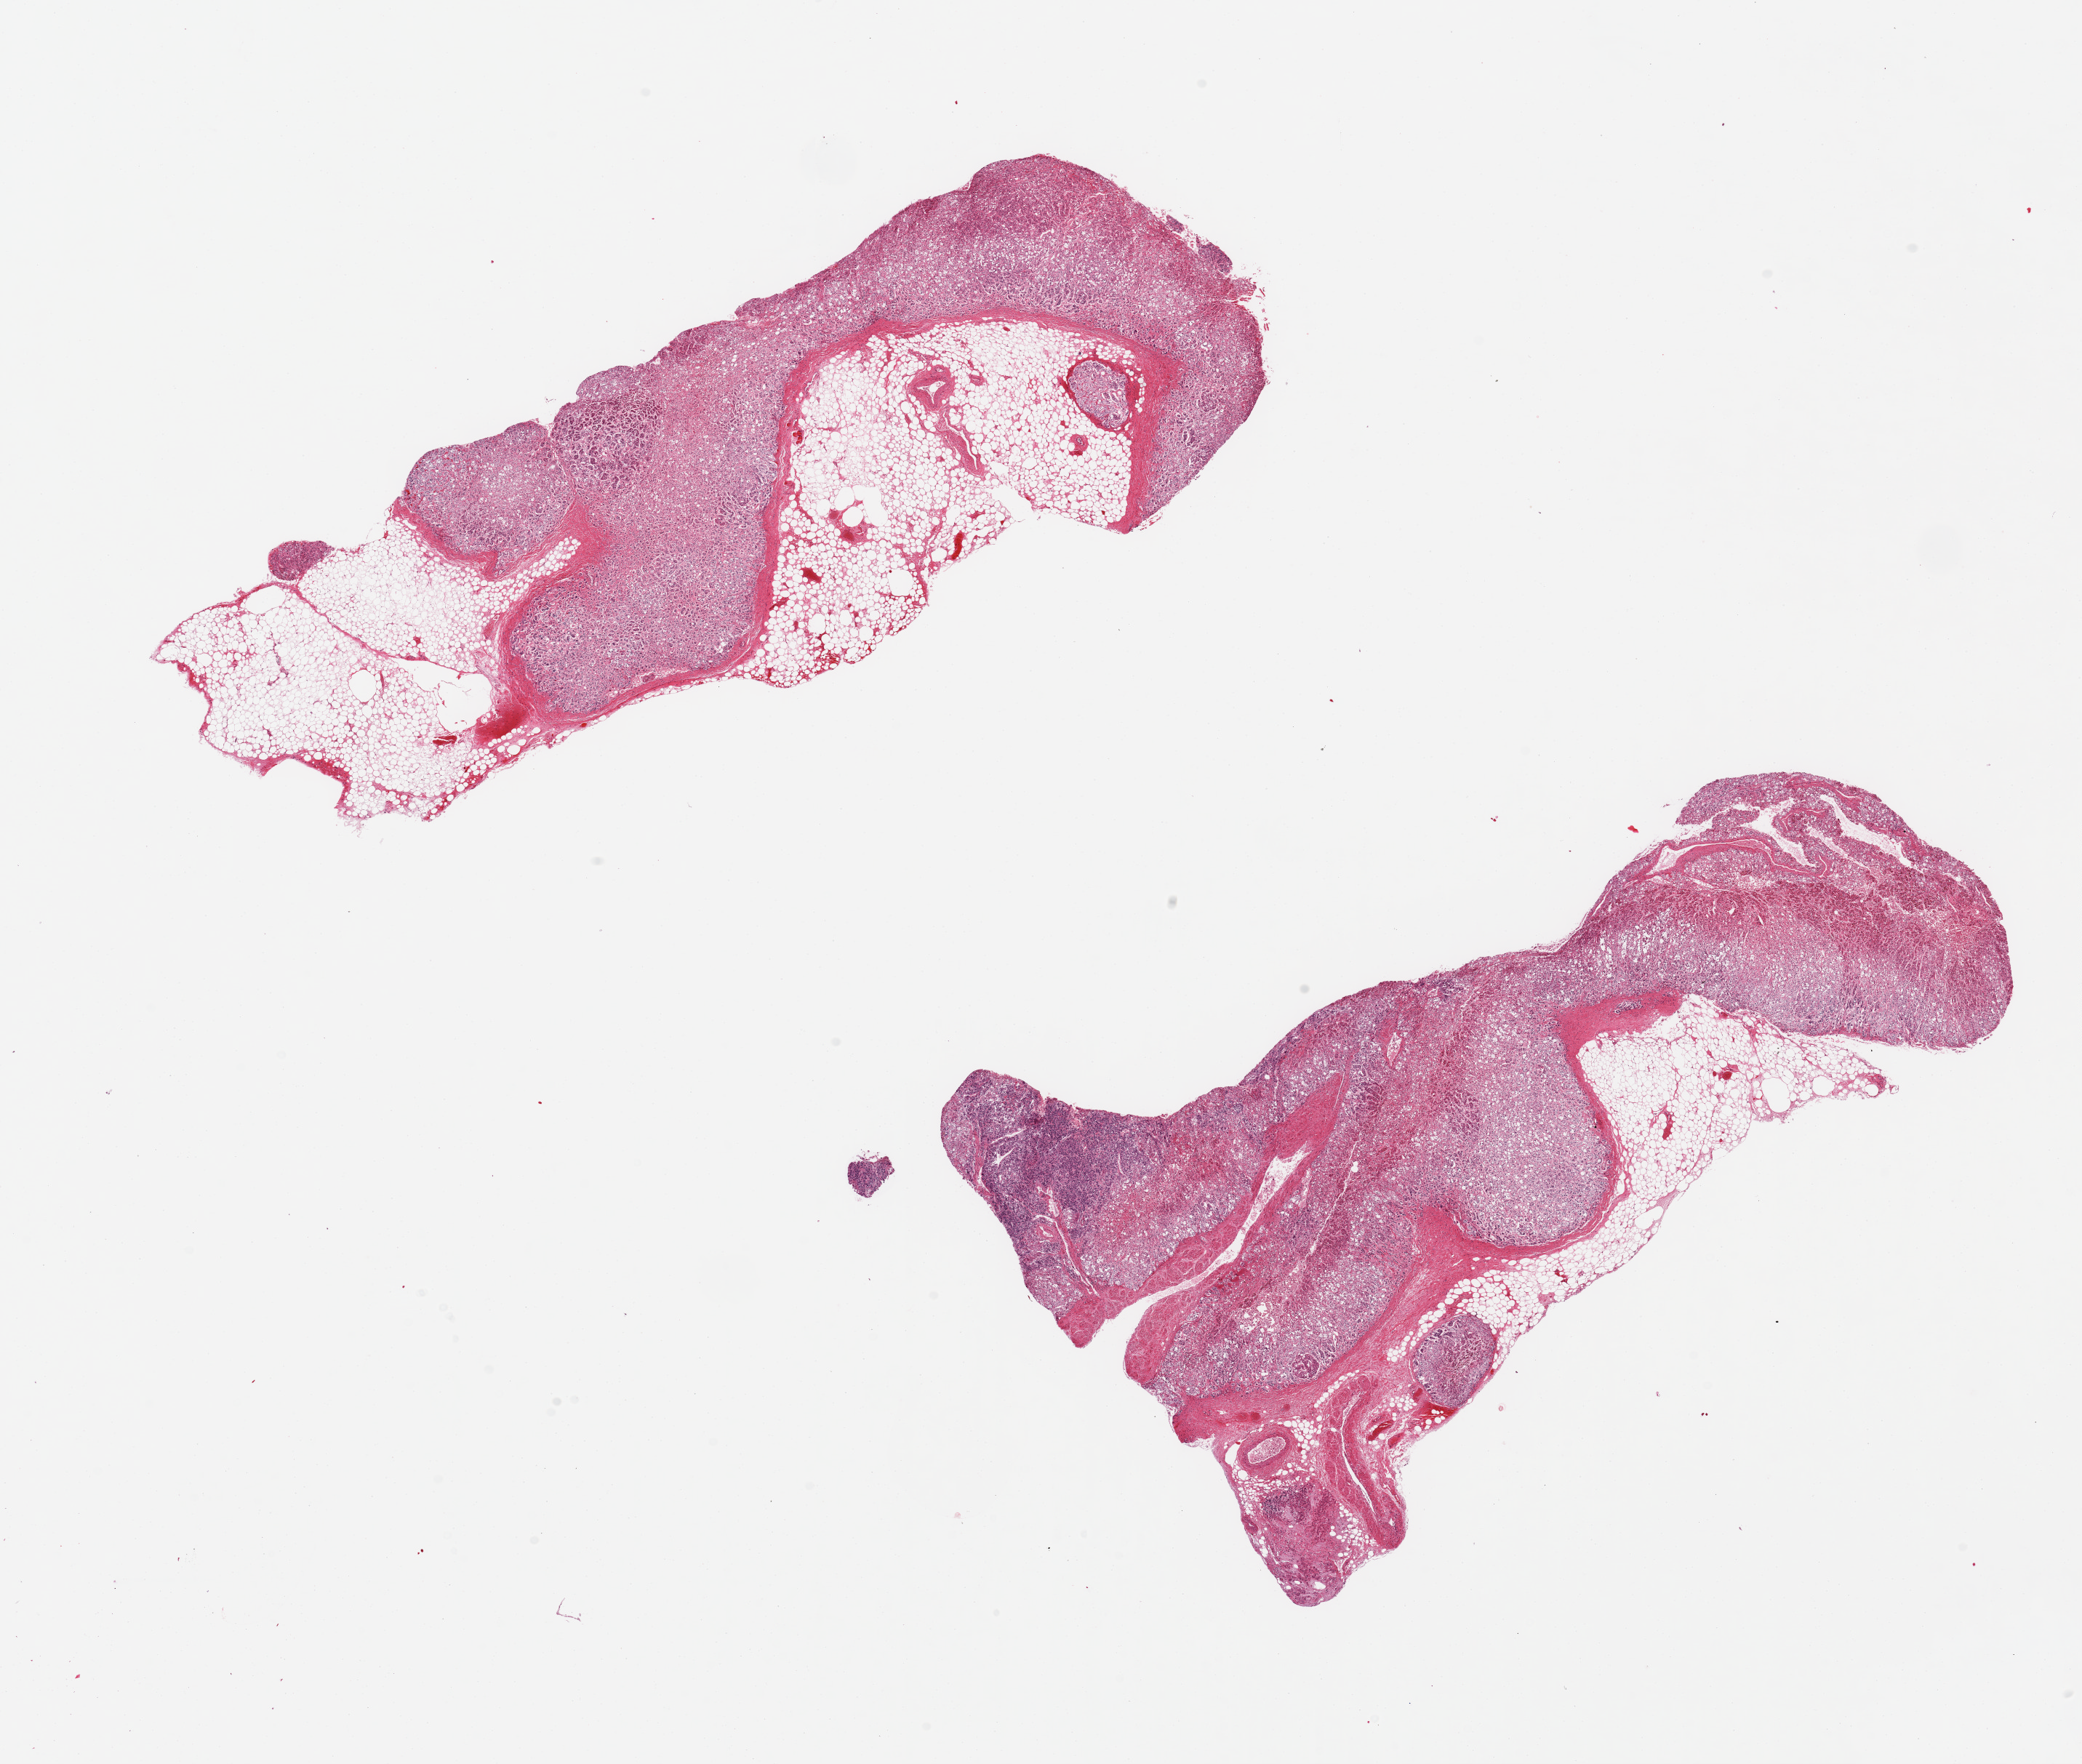
Hematoxylin and eosin (H&E) whole-slide image — low-resolution overview of the scanned area, about 22.6 x 19.2 mm, PAXgene-fixed, paraffin-embedded tissue, sampled site (target tissue): adrenal gland, tissue donor sample. Male donor.
Review note (as recorded): 2 pieces ~10x4mm, one ~50% fat, one ~20% fat.